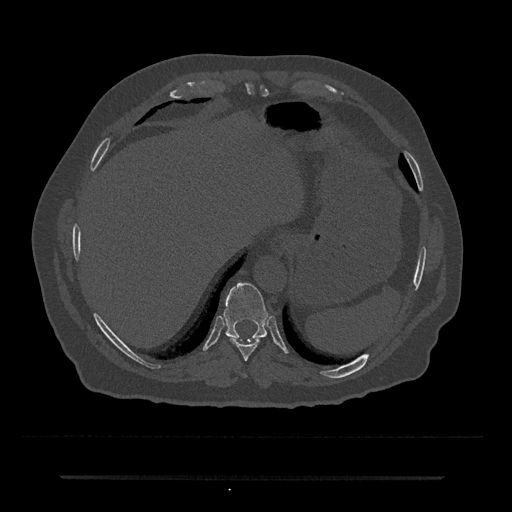
CT including the spine, one axial slice. Position 252 of 797 along the scan axis. Reconstruction kernel Br40s/3. Bone window (W 1800 / L 400 HU). 0.5 mm slice thickness. 512 × 512 image matrix, field of view 437 × 437 mm. Male patient, age 69 years. Case-level facts recorded for this patient, not image findings: primary cancer: prostate.
Outlined on this slice (semi-automatically segmented with operator editing):
- T10 vertebra: bounding box [x1, y1, x2, y2] px = [223, 283, 268, 342]
- T9 vertebra: [230, 338, 260, 361]